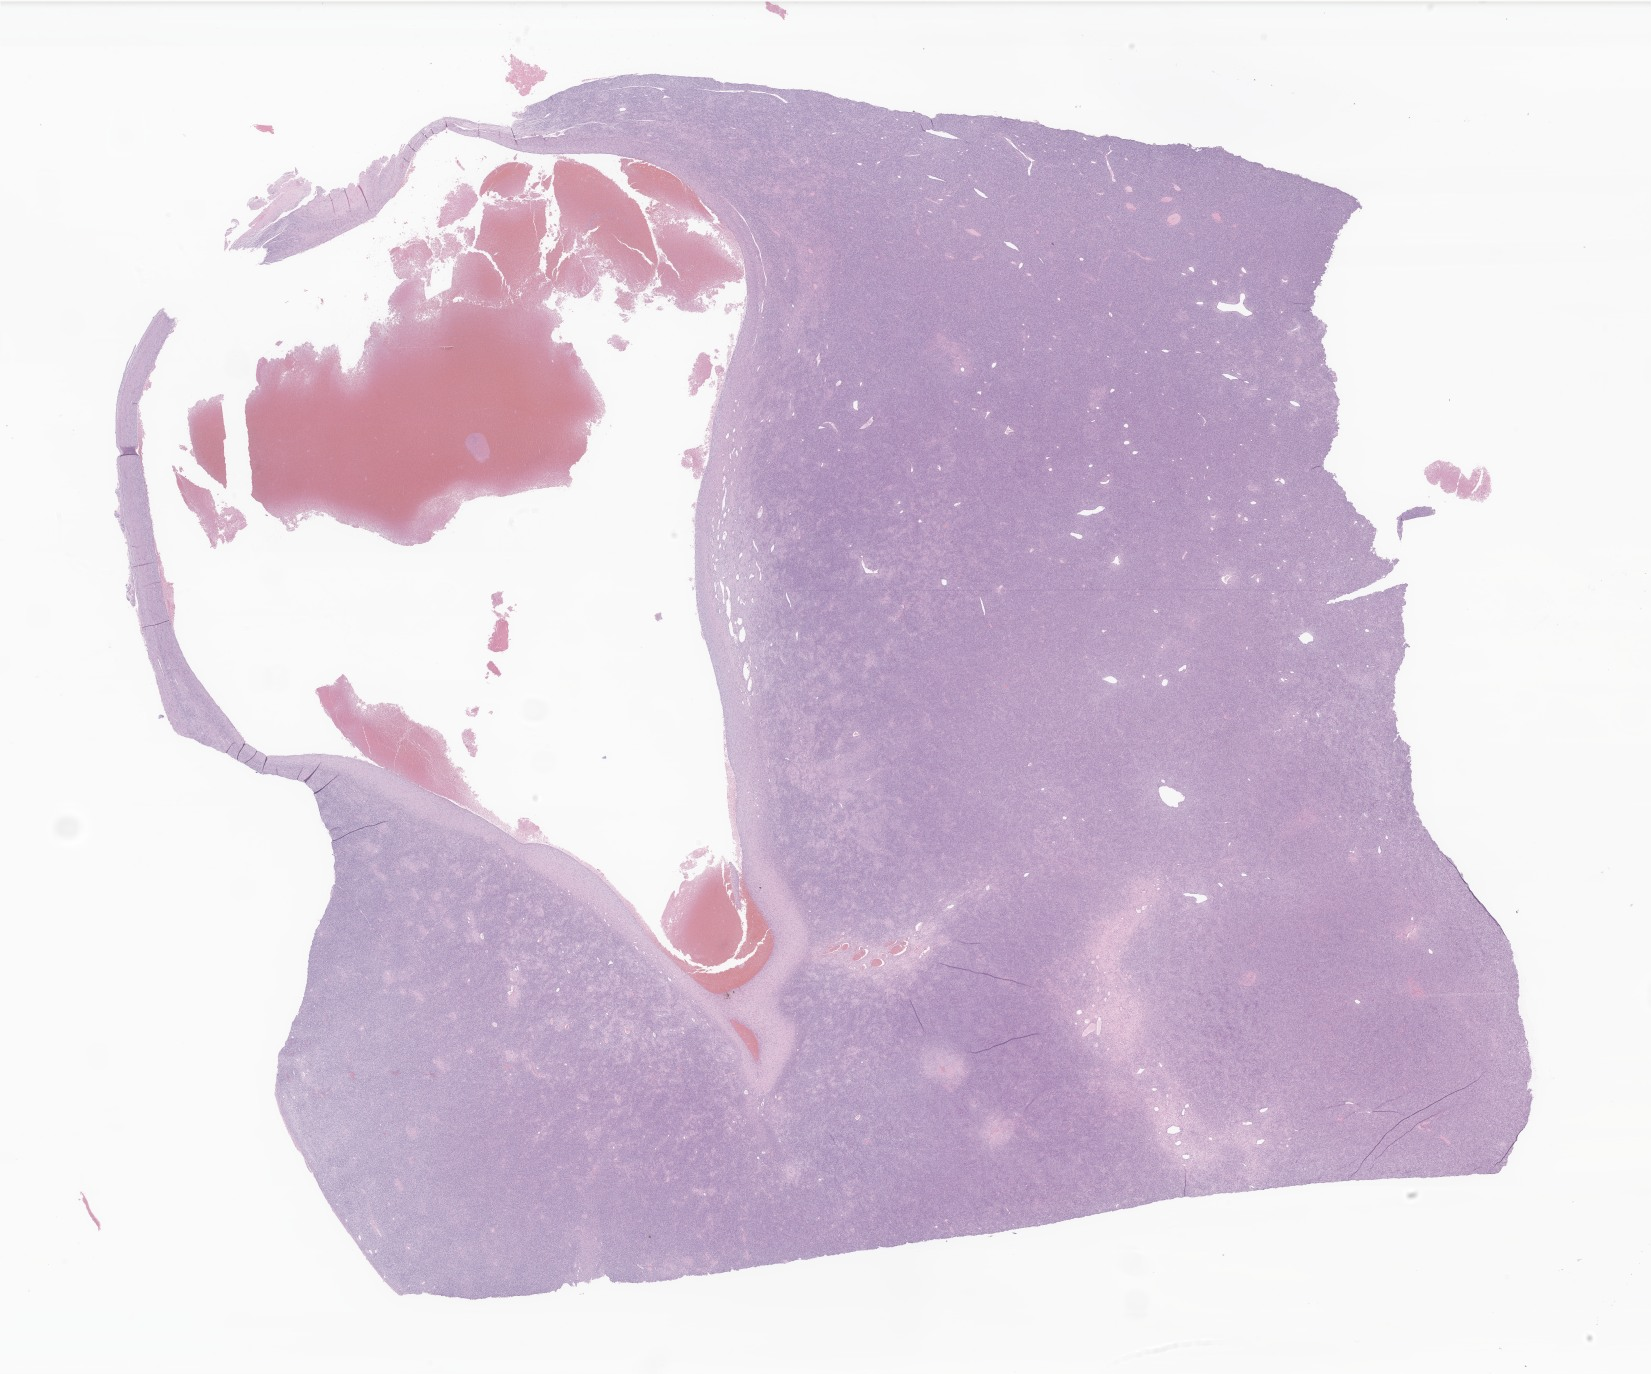
Haematoxylin and eosin whole-slide image of tumor tissue from the skin of lower limb, a low-resolution overview of the entire scanned area, about 27.8 x 23.2 mm. Formalin-fixed, paraffin-embedded (FFPE) tissue. Patient male; age 185 months (15 years 5 months).
Diagnosis (ICD-O-3 morphology term): Dermatofibrosarcoma protuberans, fibrosarcomatous.